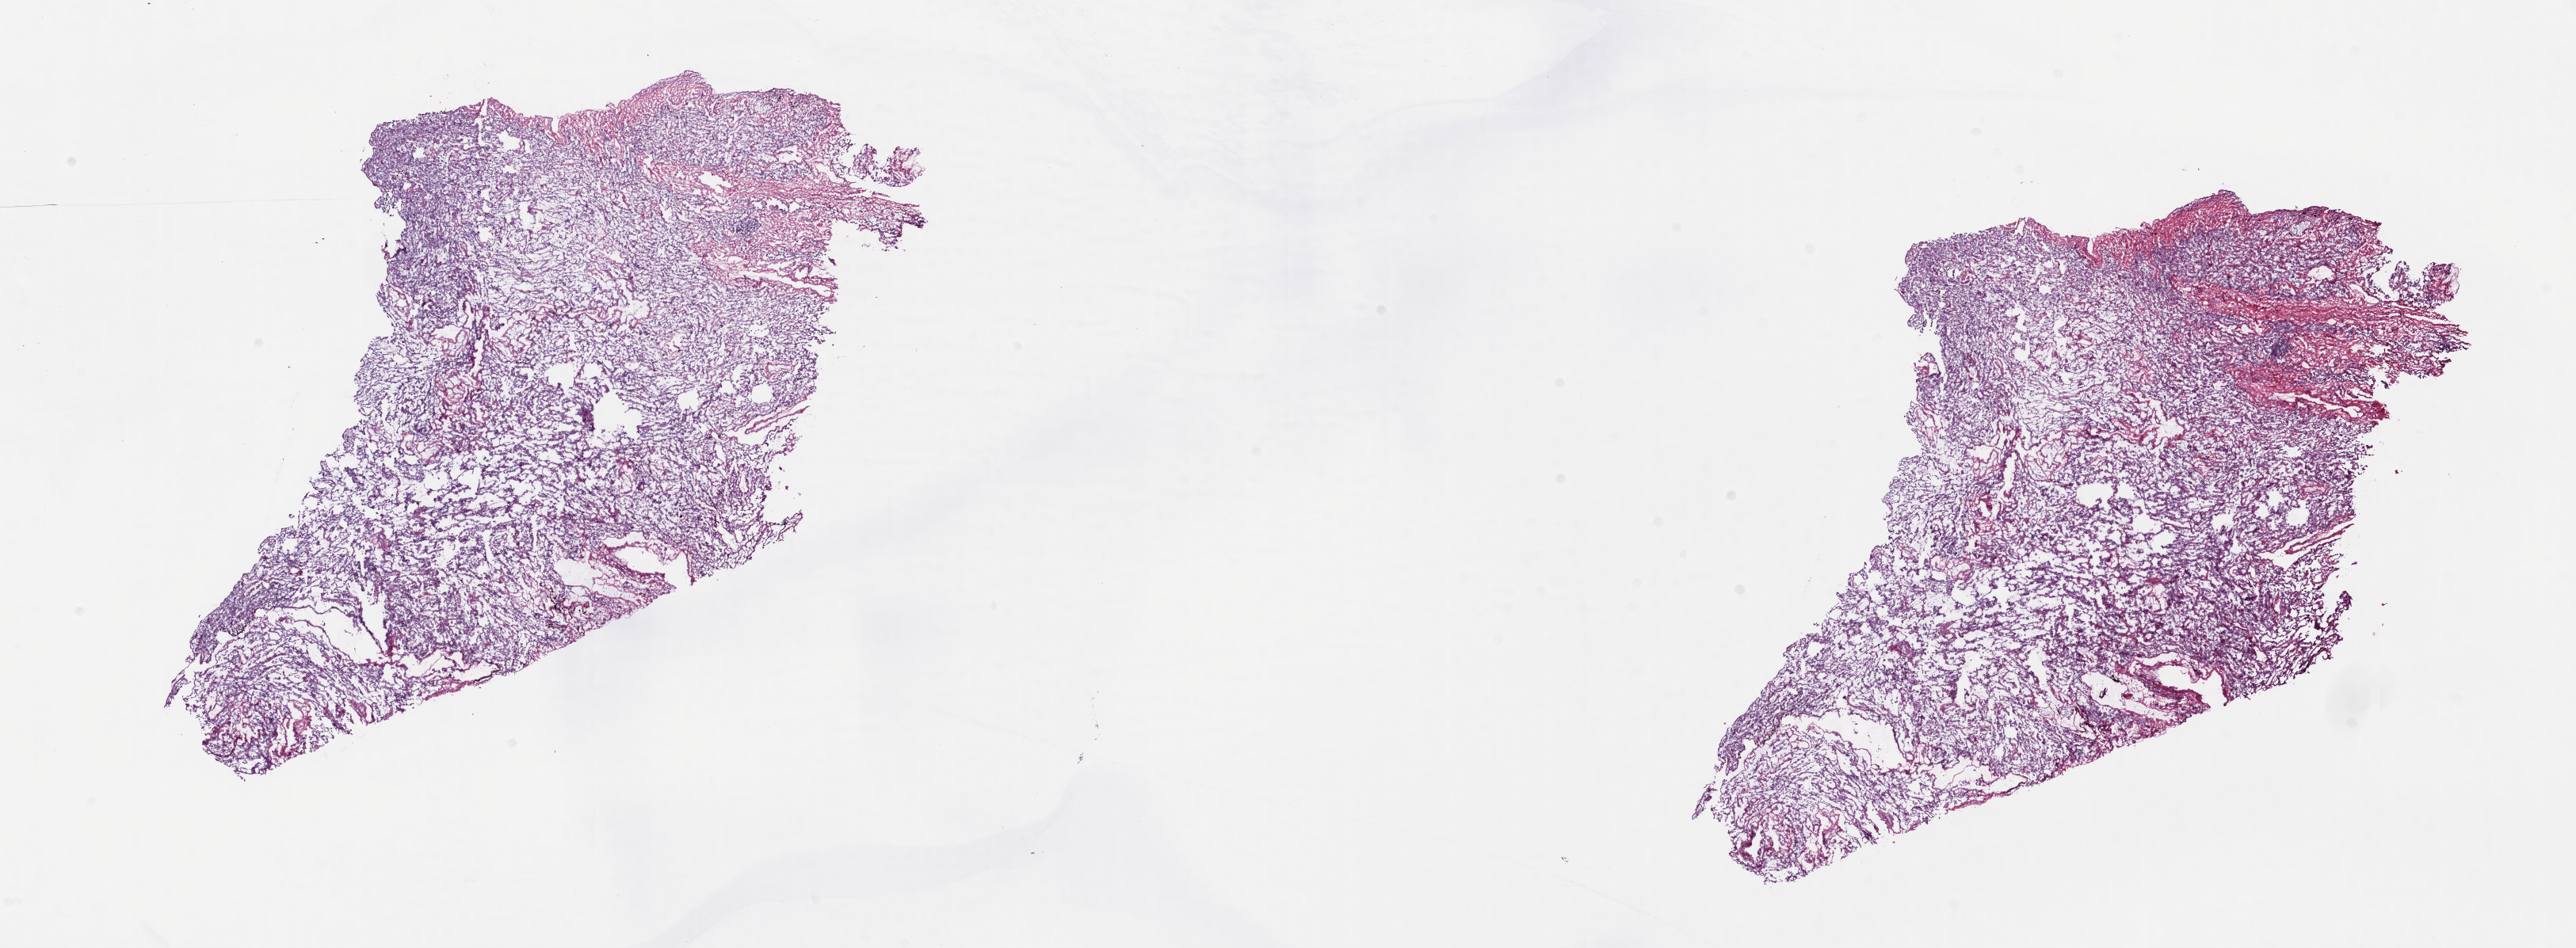
Hematoxylin and eosin (H&E) stained whole-slide image, whole scanned area (about 25.8 x 9.5 mm) shown as a low-resolution overview, frozen section, sample: solid tissue normal (non-tumour tissue), lung. Male, age 66 years at initial diagnosis. Pathologist review of this section (percent, as recorded): tumour cells 0%, tumour nuclei 0%, normal cells 60%, stromal cells 40%, necrosis 0%. Inflammatory infiltration, as recorded: lymphocyte infiltration 3%, monocyte infiltration 8%, neutrophil infiltration 3%.
* this section: solid tissue normal sample (biorepository sample class)
* patient diagnosis: Squamous cell carcinoma, NOS (upper lobe, lung)